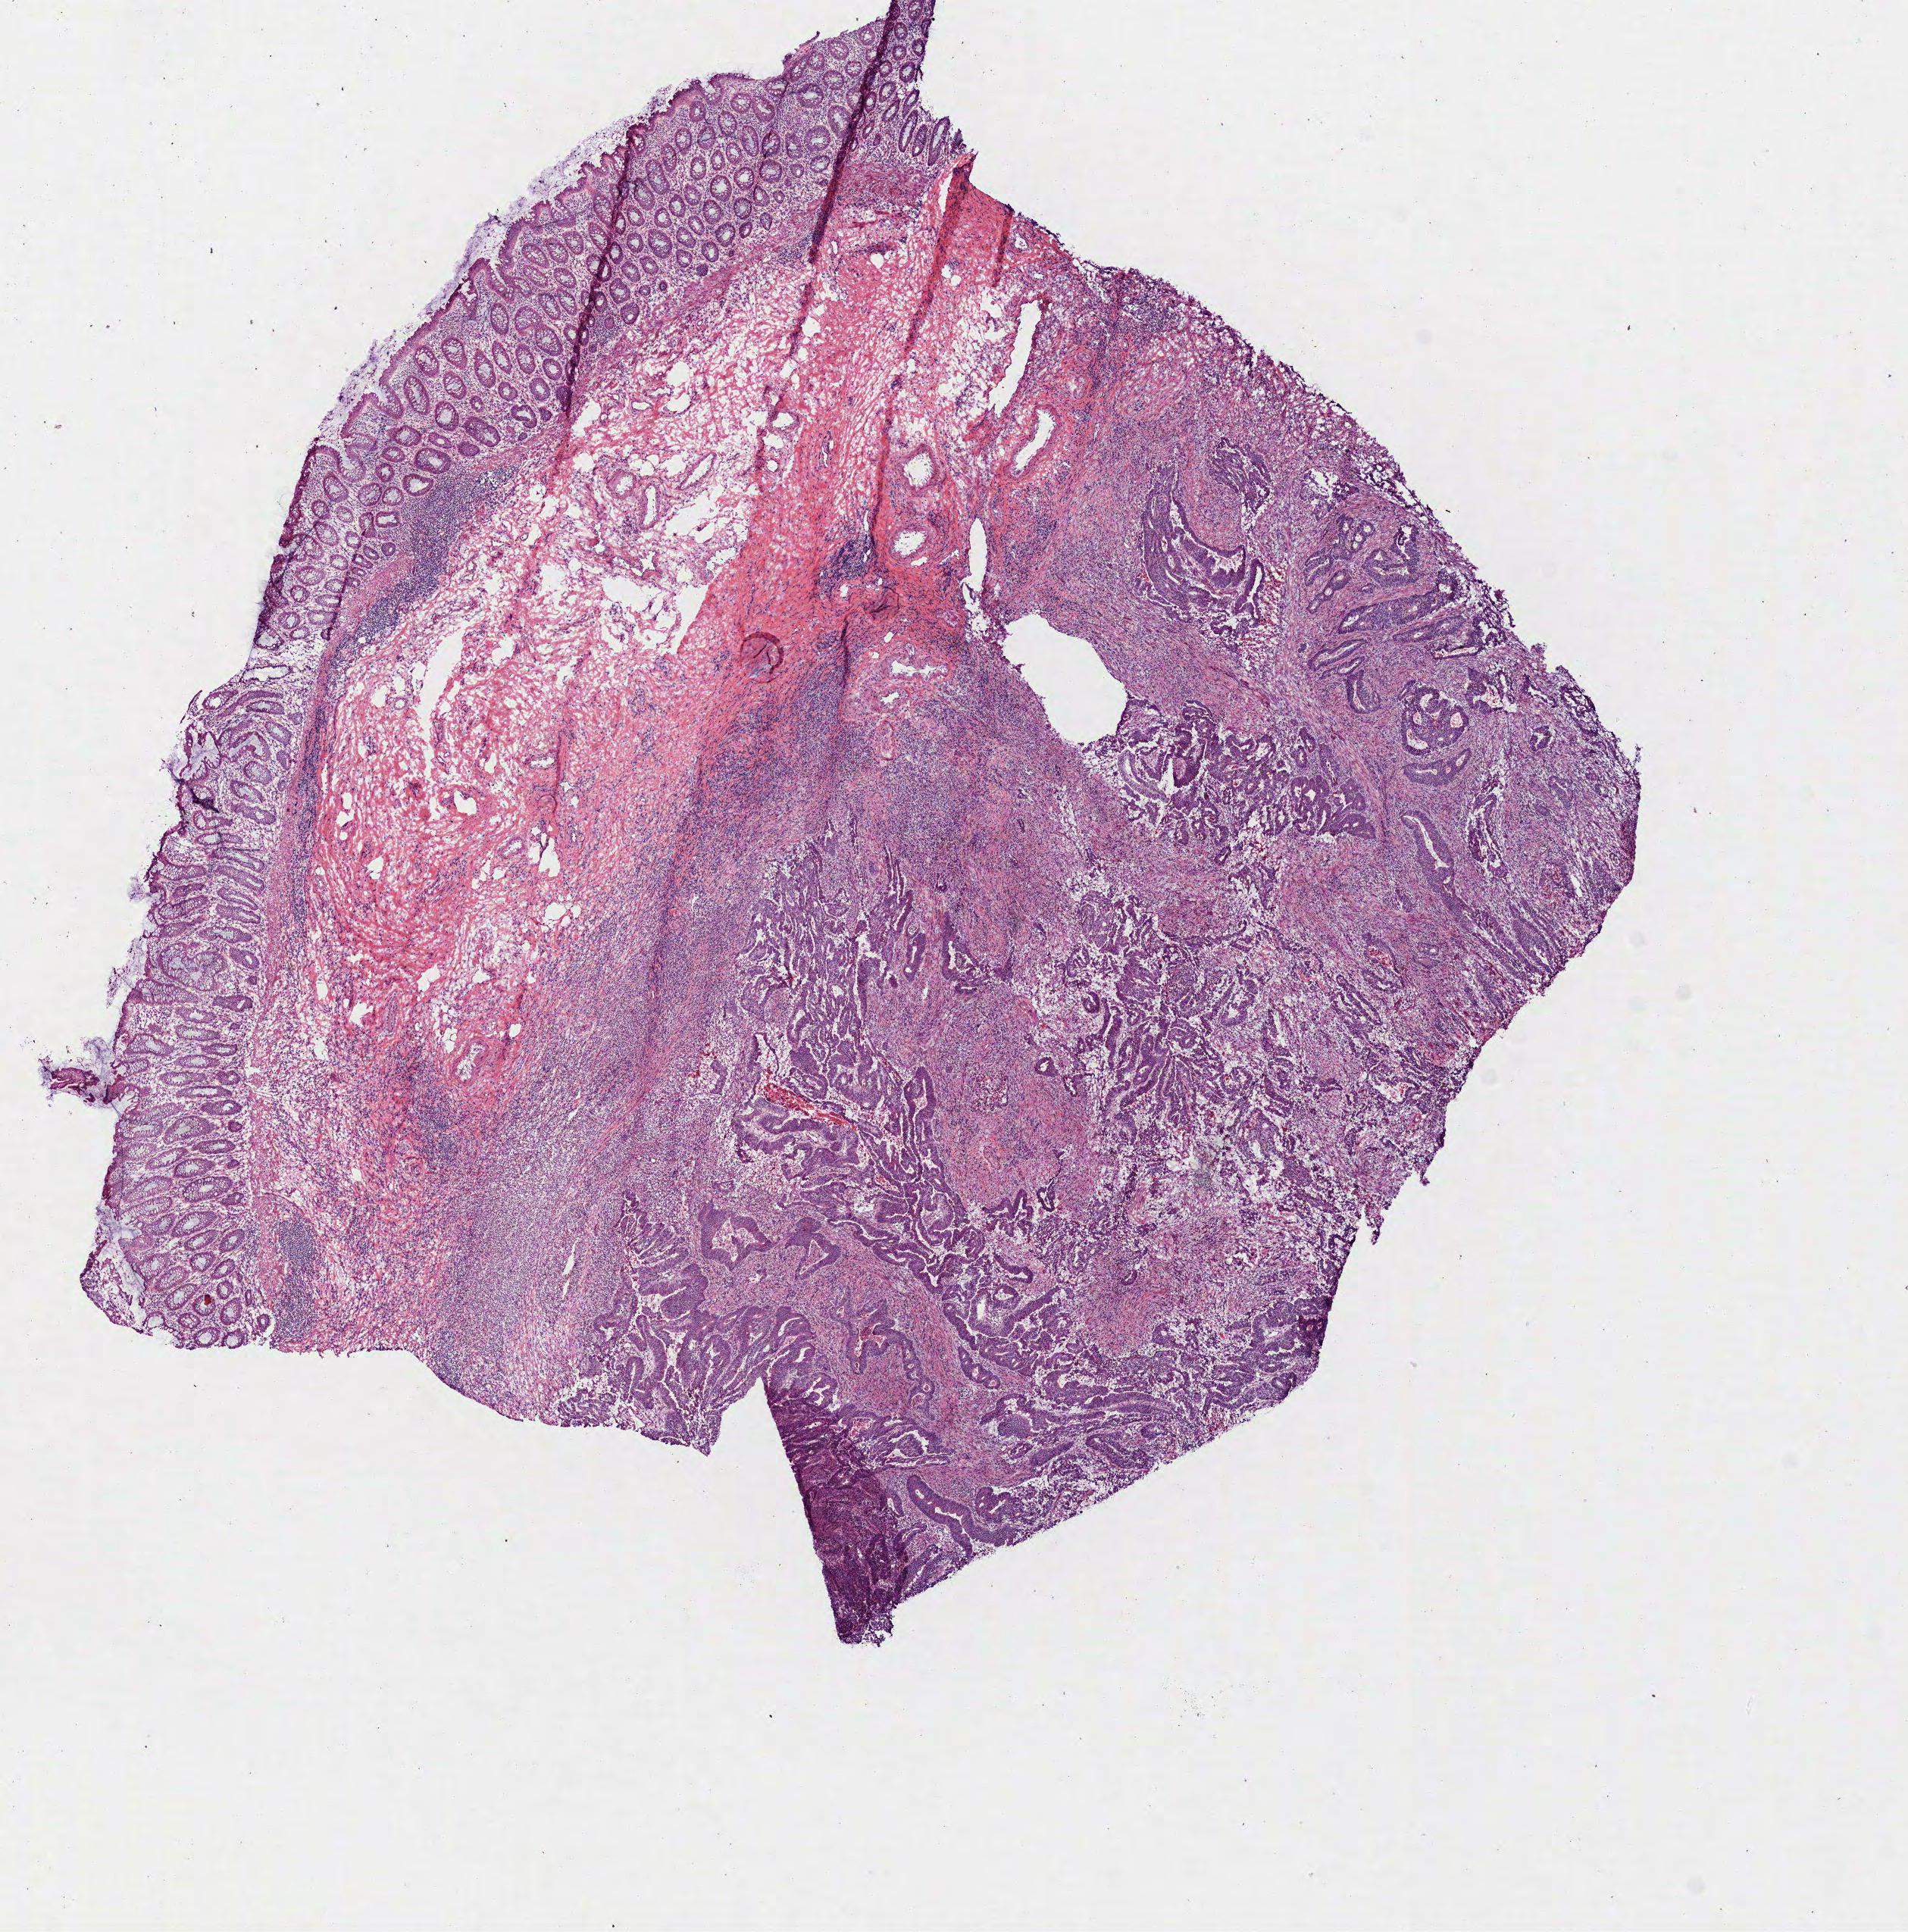
Whole-slide histology image, H&E-stained, a low-resolution overview of the entire scanned area, about 10.2 x 10.3 mm, frozen section, rectum, primary tumour sample. Patient: female, age at initial diagnosis 79 years.
Histologic diagnosis: Adenocarcinoma, NOS (rectosigmoid junction).